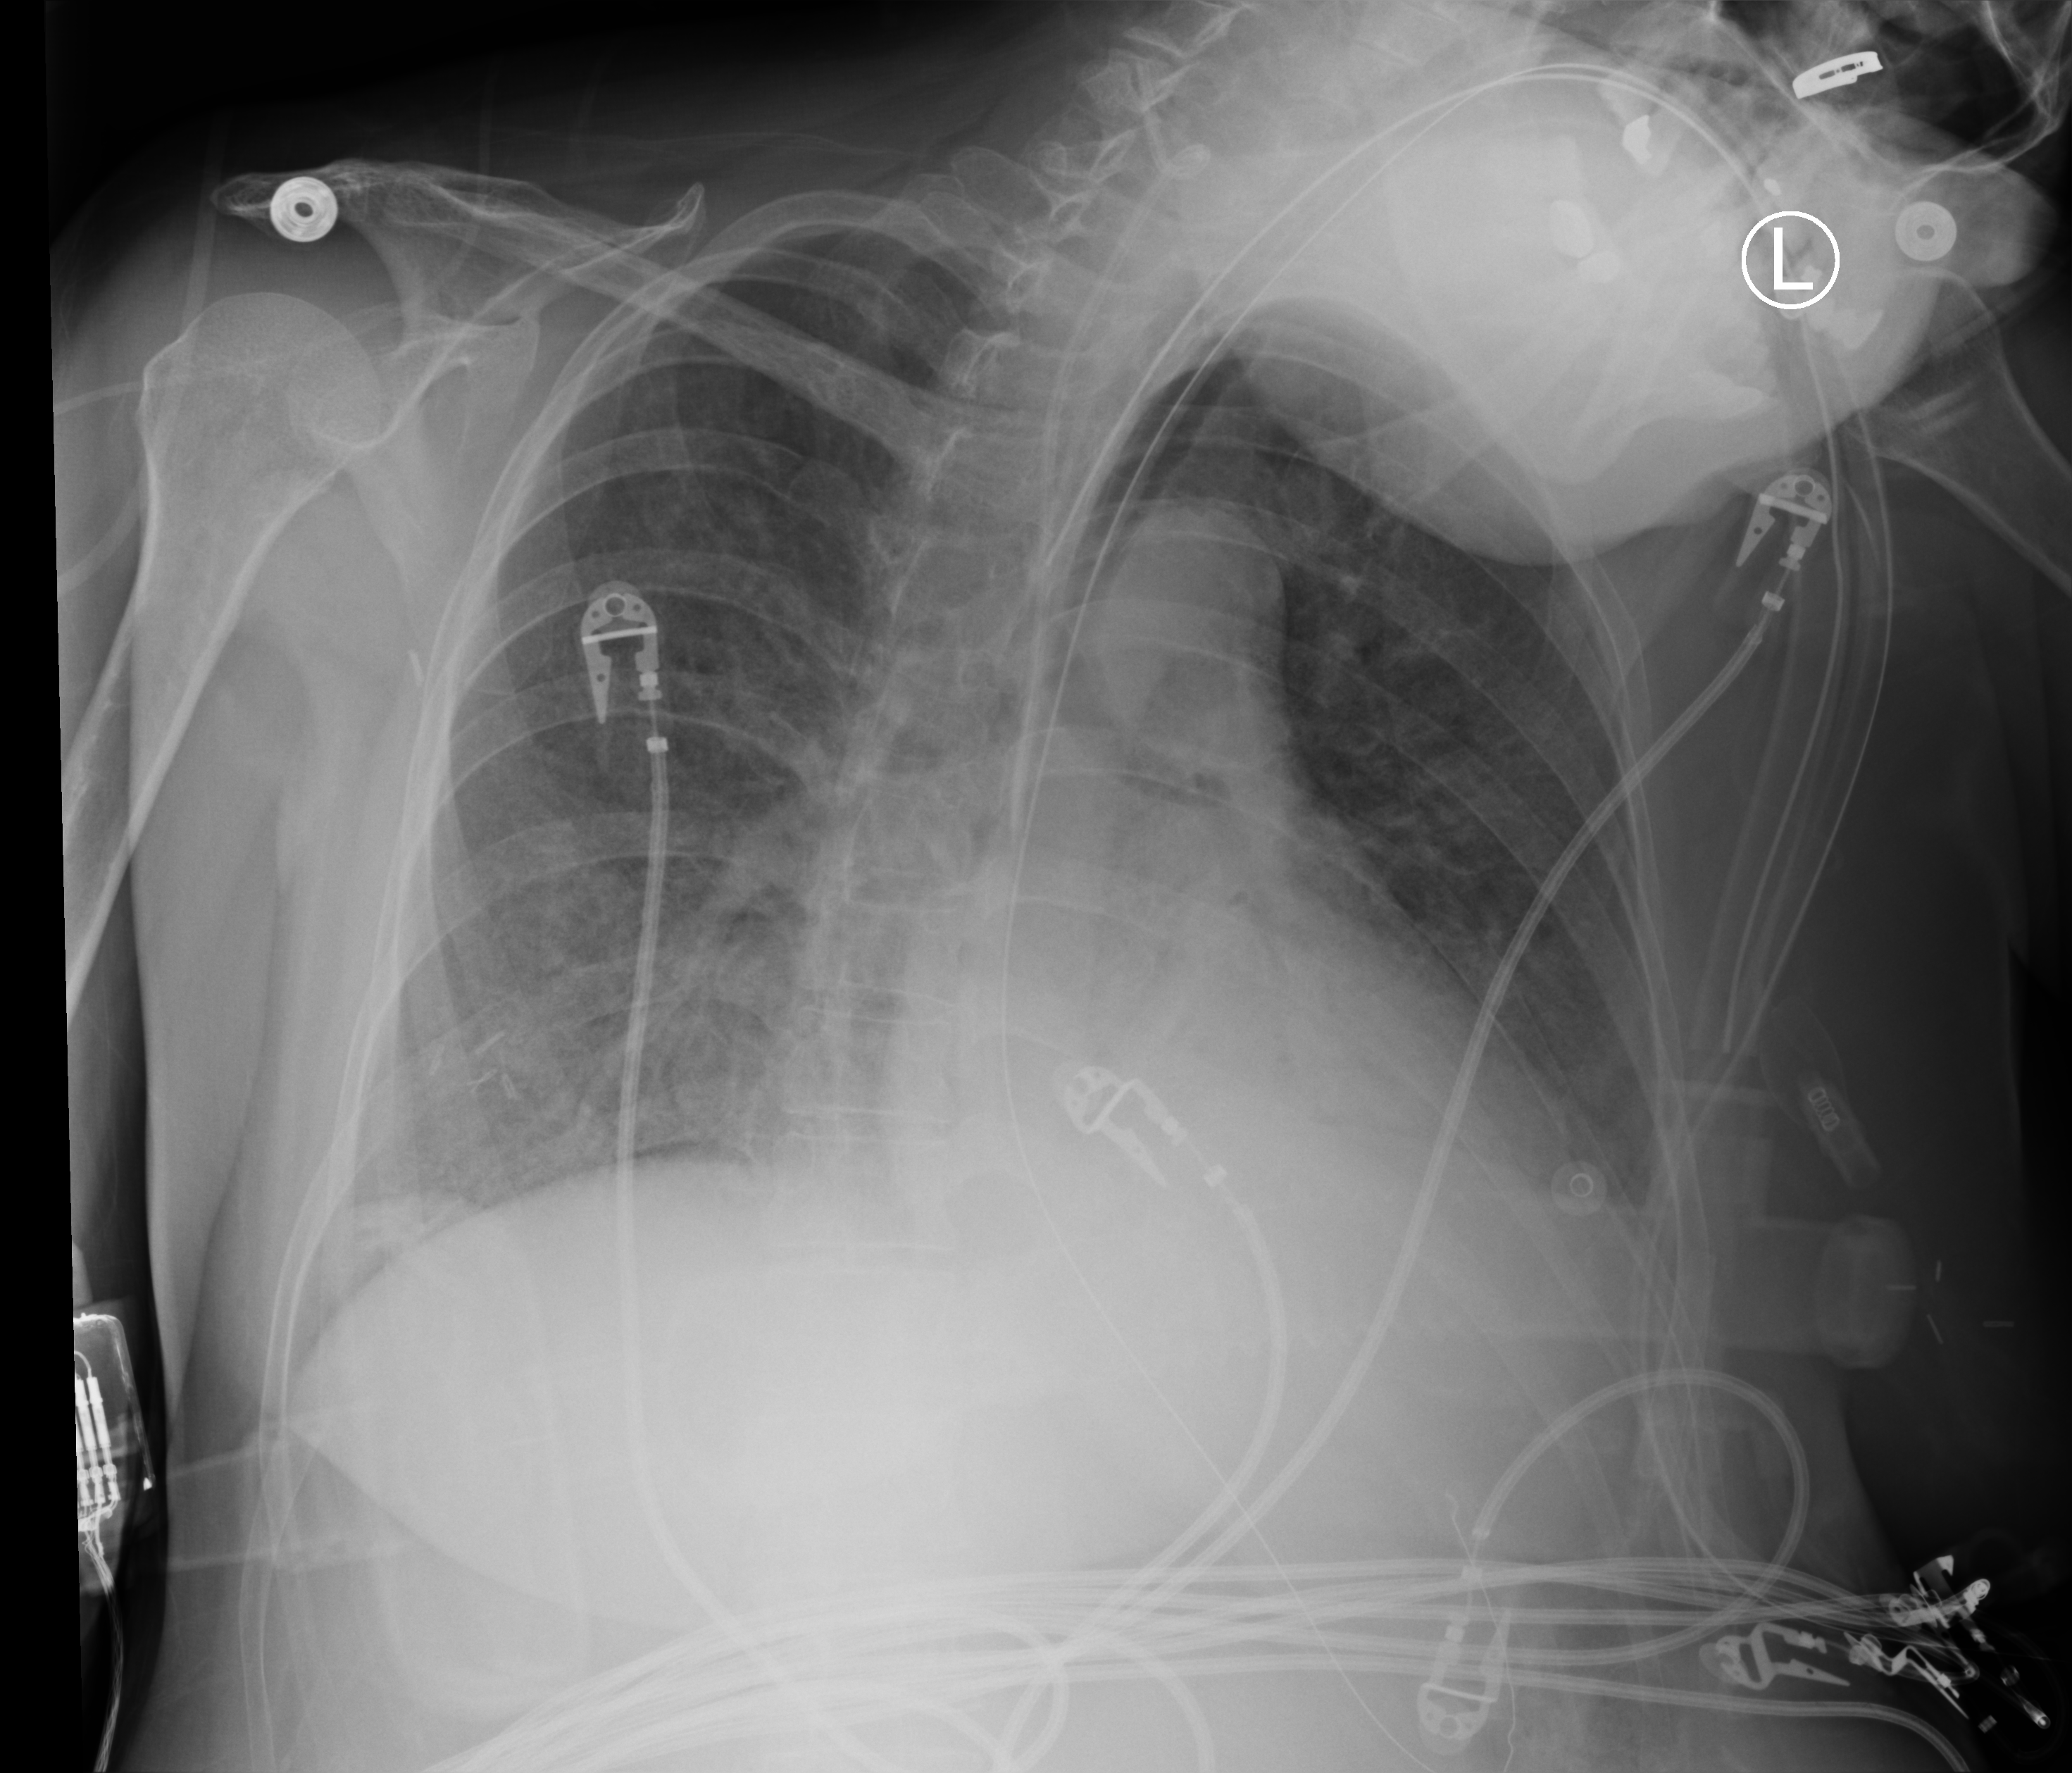
Bedside chest radiograph (computed radiography); anteroposterior (AP) projection. Patient hospitalised with COVID-19; female, aged 18–59 years.
From the hospital-stay record, not from the radiograph (when in the stay this image was taken is not recorded):
- other chronic lung disease (admission record): no
- chronic kidney disease (admission record): no
- admitted to intensive care during this hospital stay: no